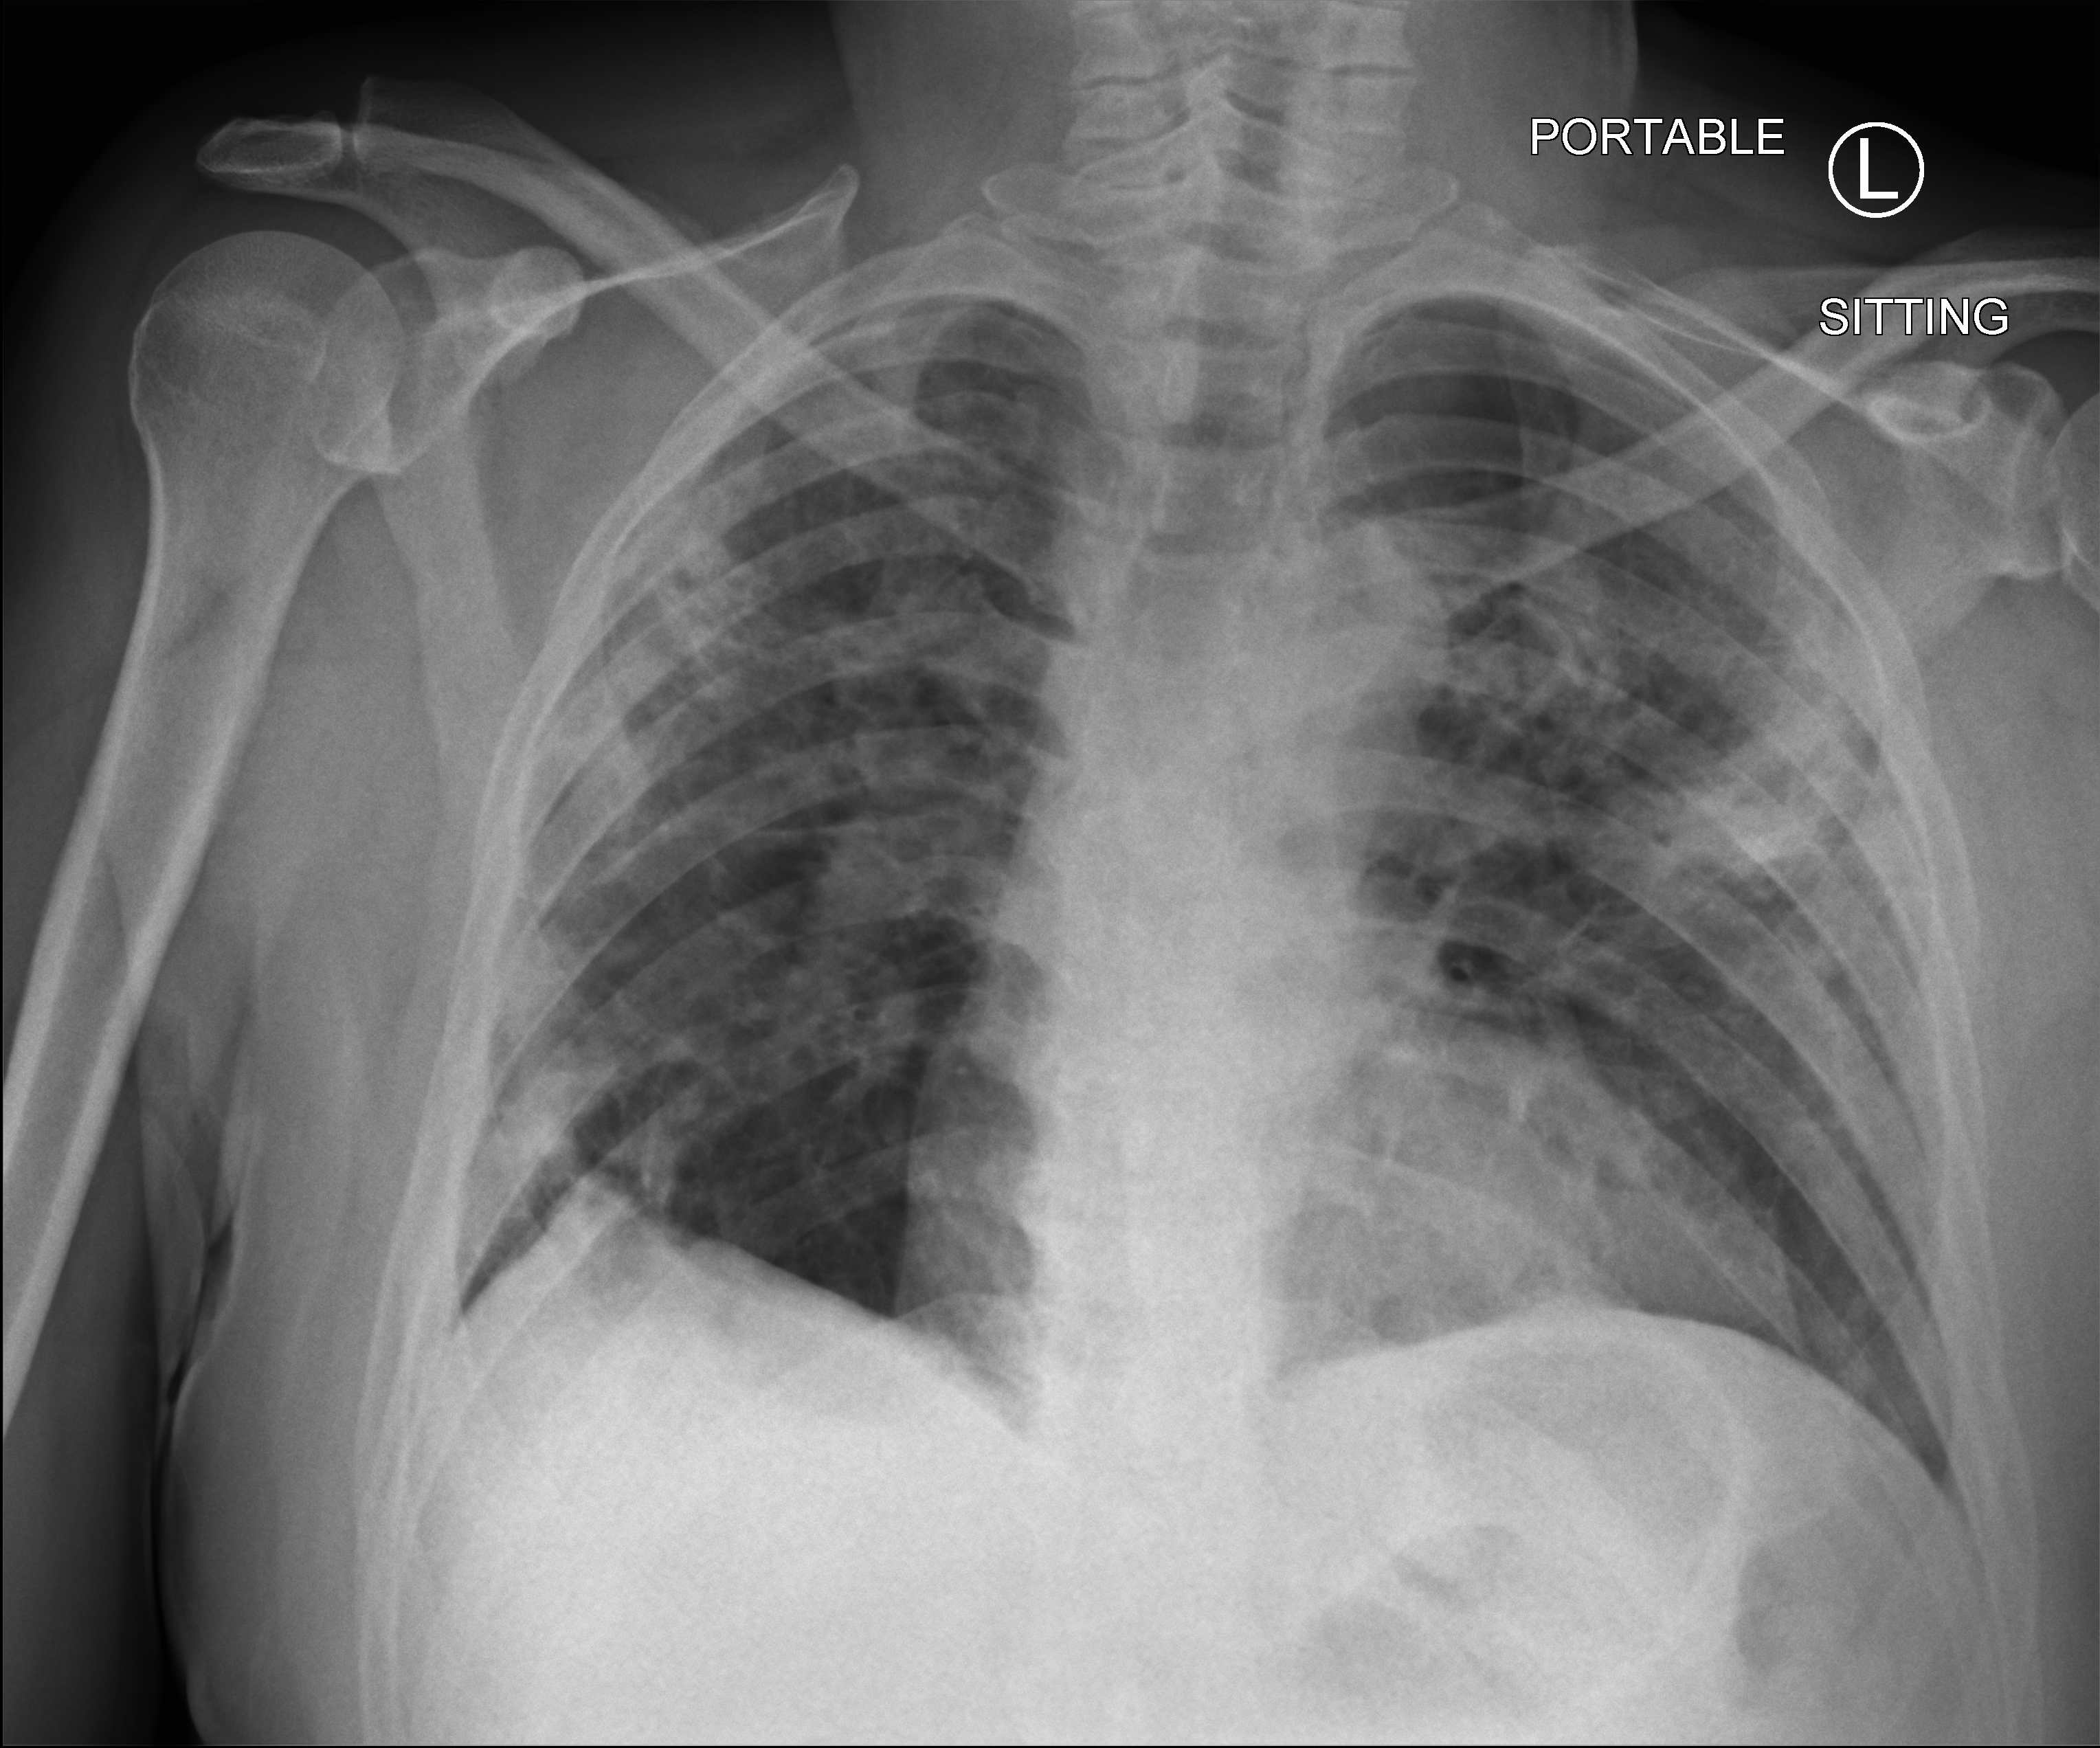
Chest X-ray (portable), anteroposterior (AP) projection. Male patient hospitalised with COVID-19, age 18–59 years.
Admission-level facts for this patient (not findings on this image; timing relative to this image not recorded): mechanically ventilated during this hospital stay: no; hypertension (admission record): no; admitted to intensive care during this hospital stay: no.